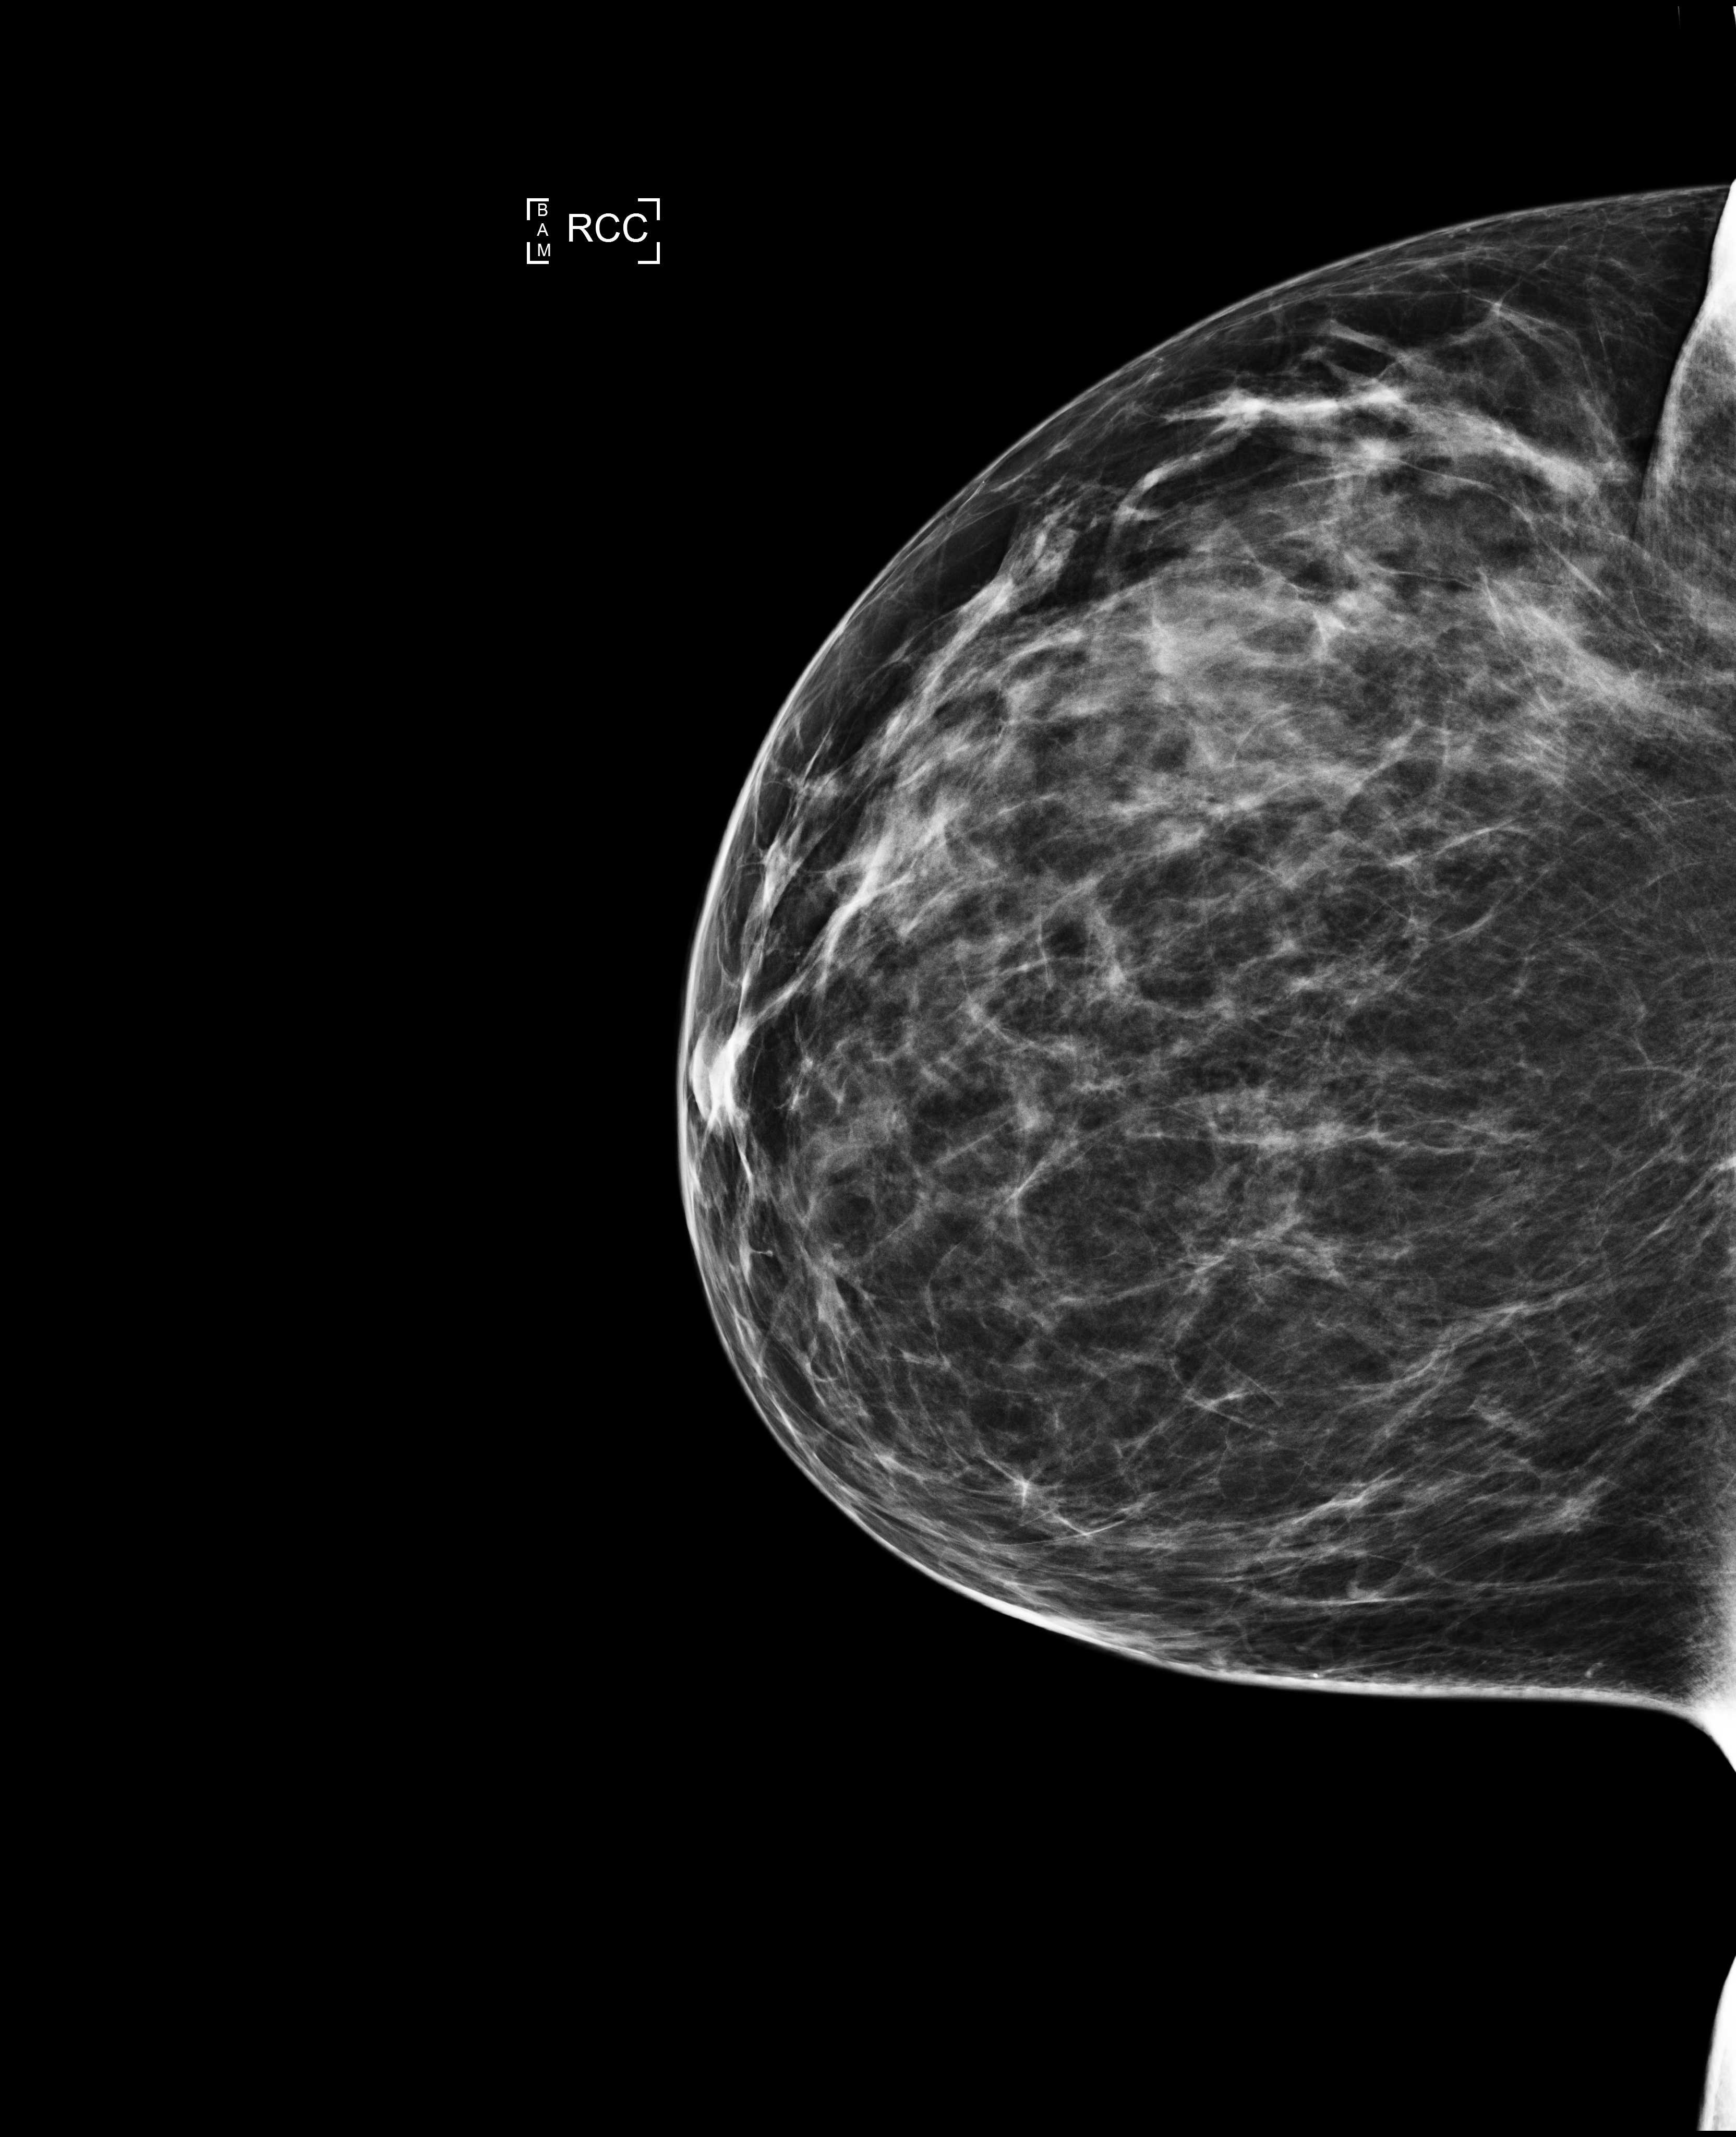
Screening examination. Patient aged 42 years (female).
Image type: full-field digital mammogram. Breast: right. Projection: CC view. Breast density at the screening exam (both breasts): heterogeneously dense (BI-RADS density category c). Final BI-RADS assessment for this screening round (tomosynthesis exam, both breasts): category 1. Recall: no recall after this screen.